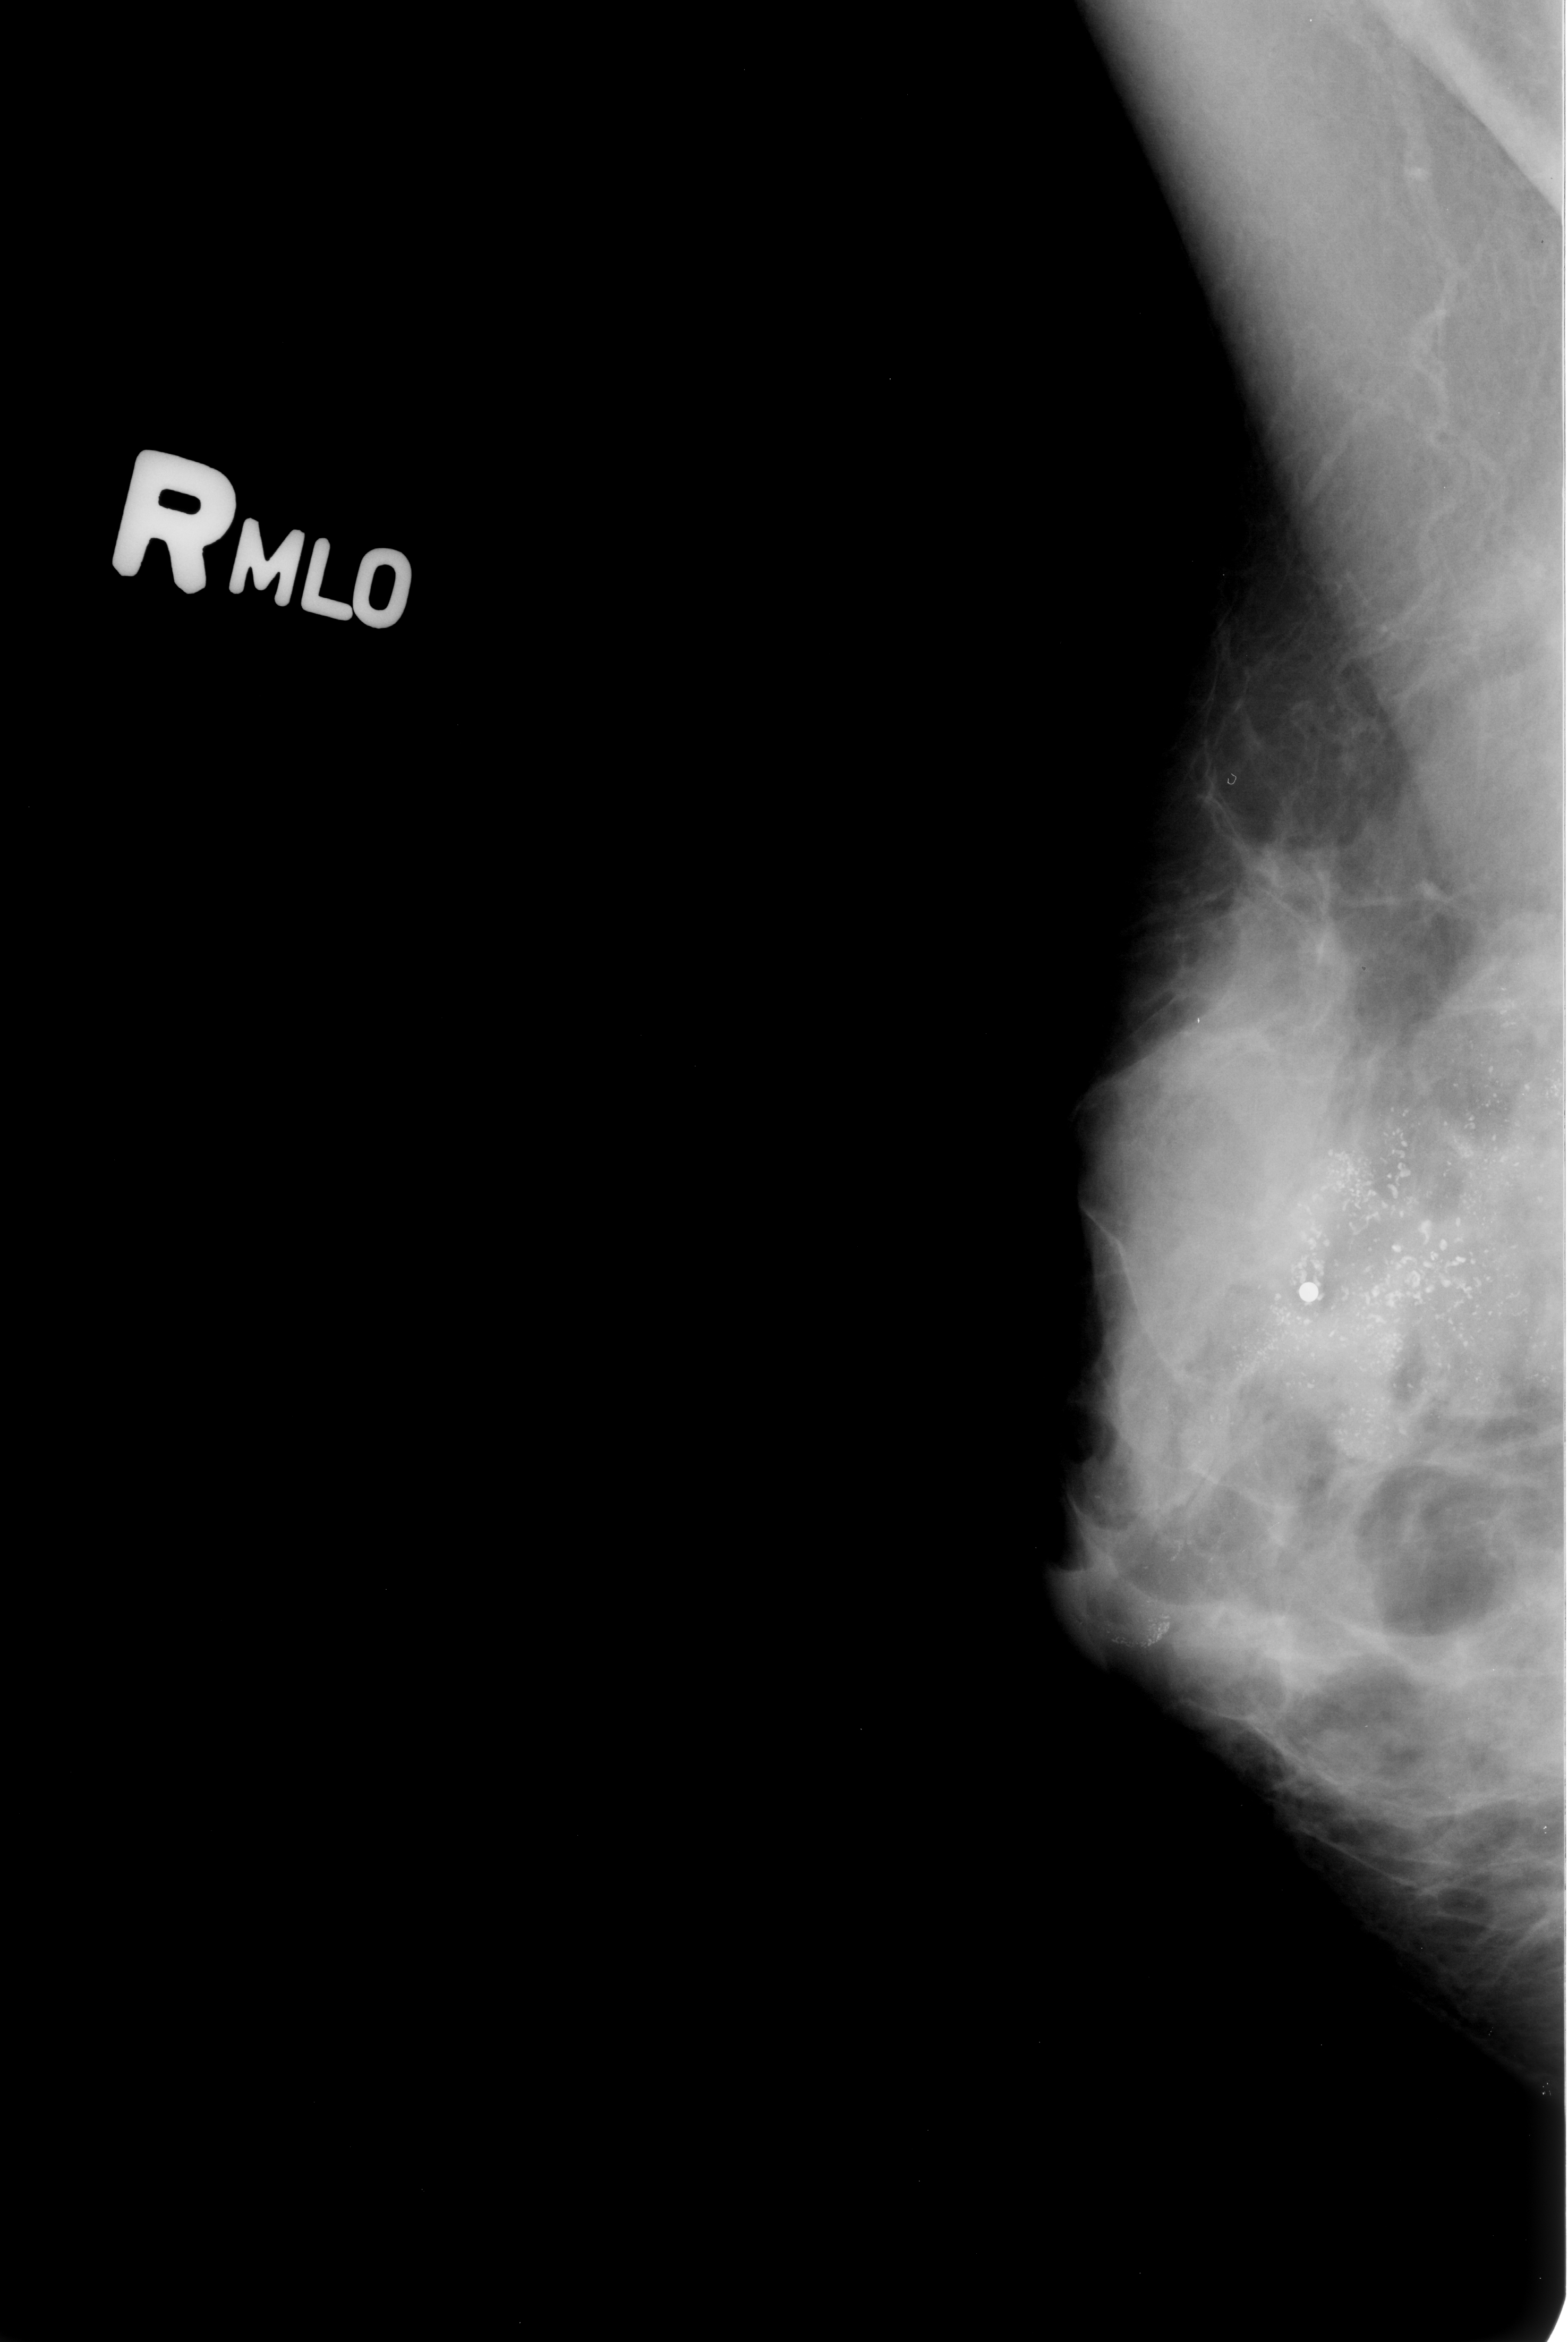
Scanned film-screen mammogram, right breast, mediolateral oblique (MLO) view, BI-RADS breast density category 3 (scale 1–4).
- Marked findings (only marked abnormalities are described; nothing is implied about the rest of the image): calcifications, morphology pleomorphic, distribution regional; BI-RADS assessment category 5; subtlety rating 5 on a 1 (subtle) to 5 (obvious) scale; pathology (as recorded): malignant.